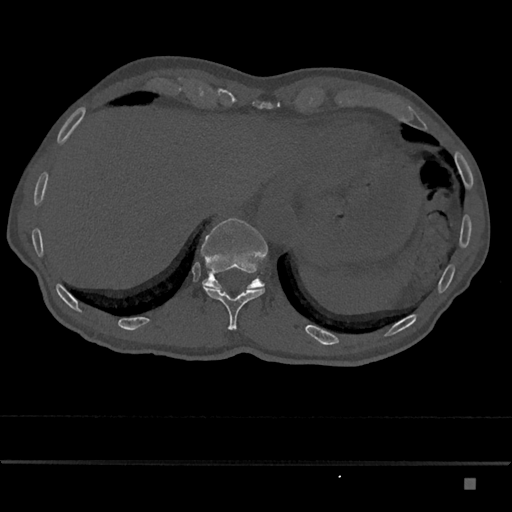
CT including the spine, one axial slice; slice 653 of 797 in the series (ordered by position); bone window (W 1800 / L 400 HU); 512 × 512 image matrix, field of view 390 × 390 mm. Patient: male, 72 years. Case-level facts recorded for this patient, not image findings: primary cancer: prostate.
Annotated regions visible in this slice (semi-automatic segmentation, software-assisted and operator-edited):
- T11 vertebra: box from (x=202, y=283) to (x=265, y=330) px
- T12 vertebra: (x=201, y=218)–(x=268, y=289)